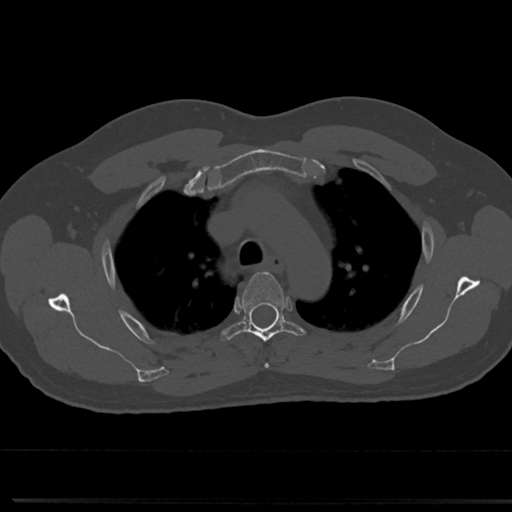
CT including the spine, one axial slice. Slice 553 of 817 in the series (ordered by position). Reconstruction kernel Br40s/3. 120 kVp. Bone window (W 1800 / L 400 HU). 0.5 mm slice thickness. 512 × 512 image matrix, field of view 355 × 355 mm. Patient: male, 61 years. Case-level facts recorded for this patient, not image findings: primary cancer: prostate.
Structures marked on this image (semi-automatic segmentation, software-assisted and operator-edited):
- T3 vertebra: bounding box (x1, y1, x2, y2) in pixels: (264, 363, 269, 368)
- T4 vertebra: (219, 272, 306, 343)